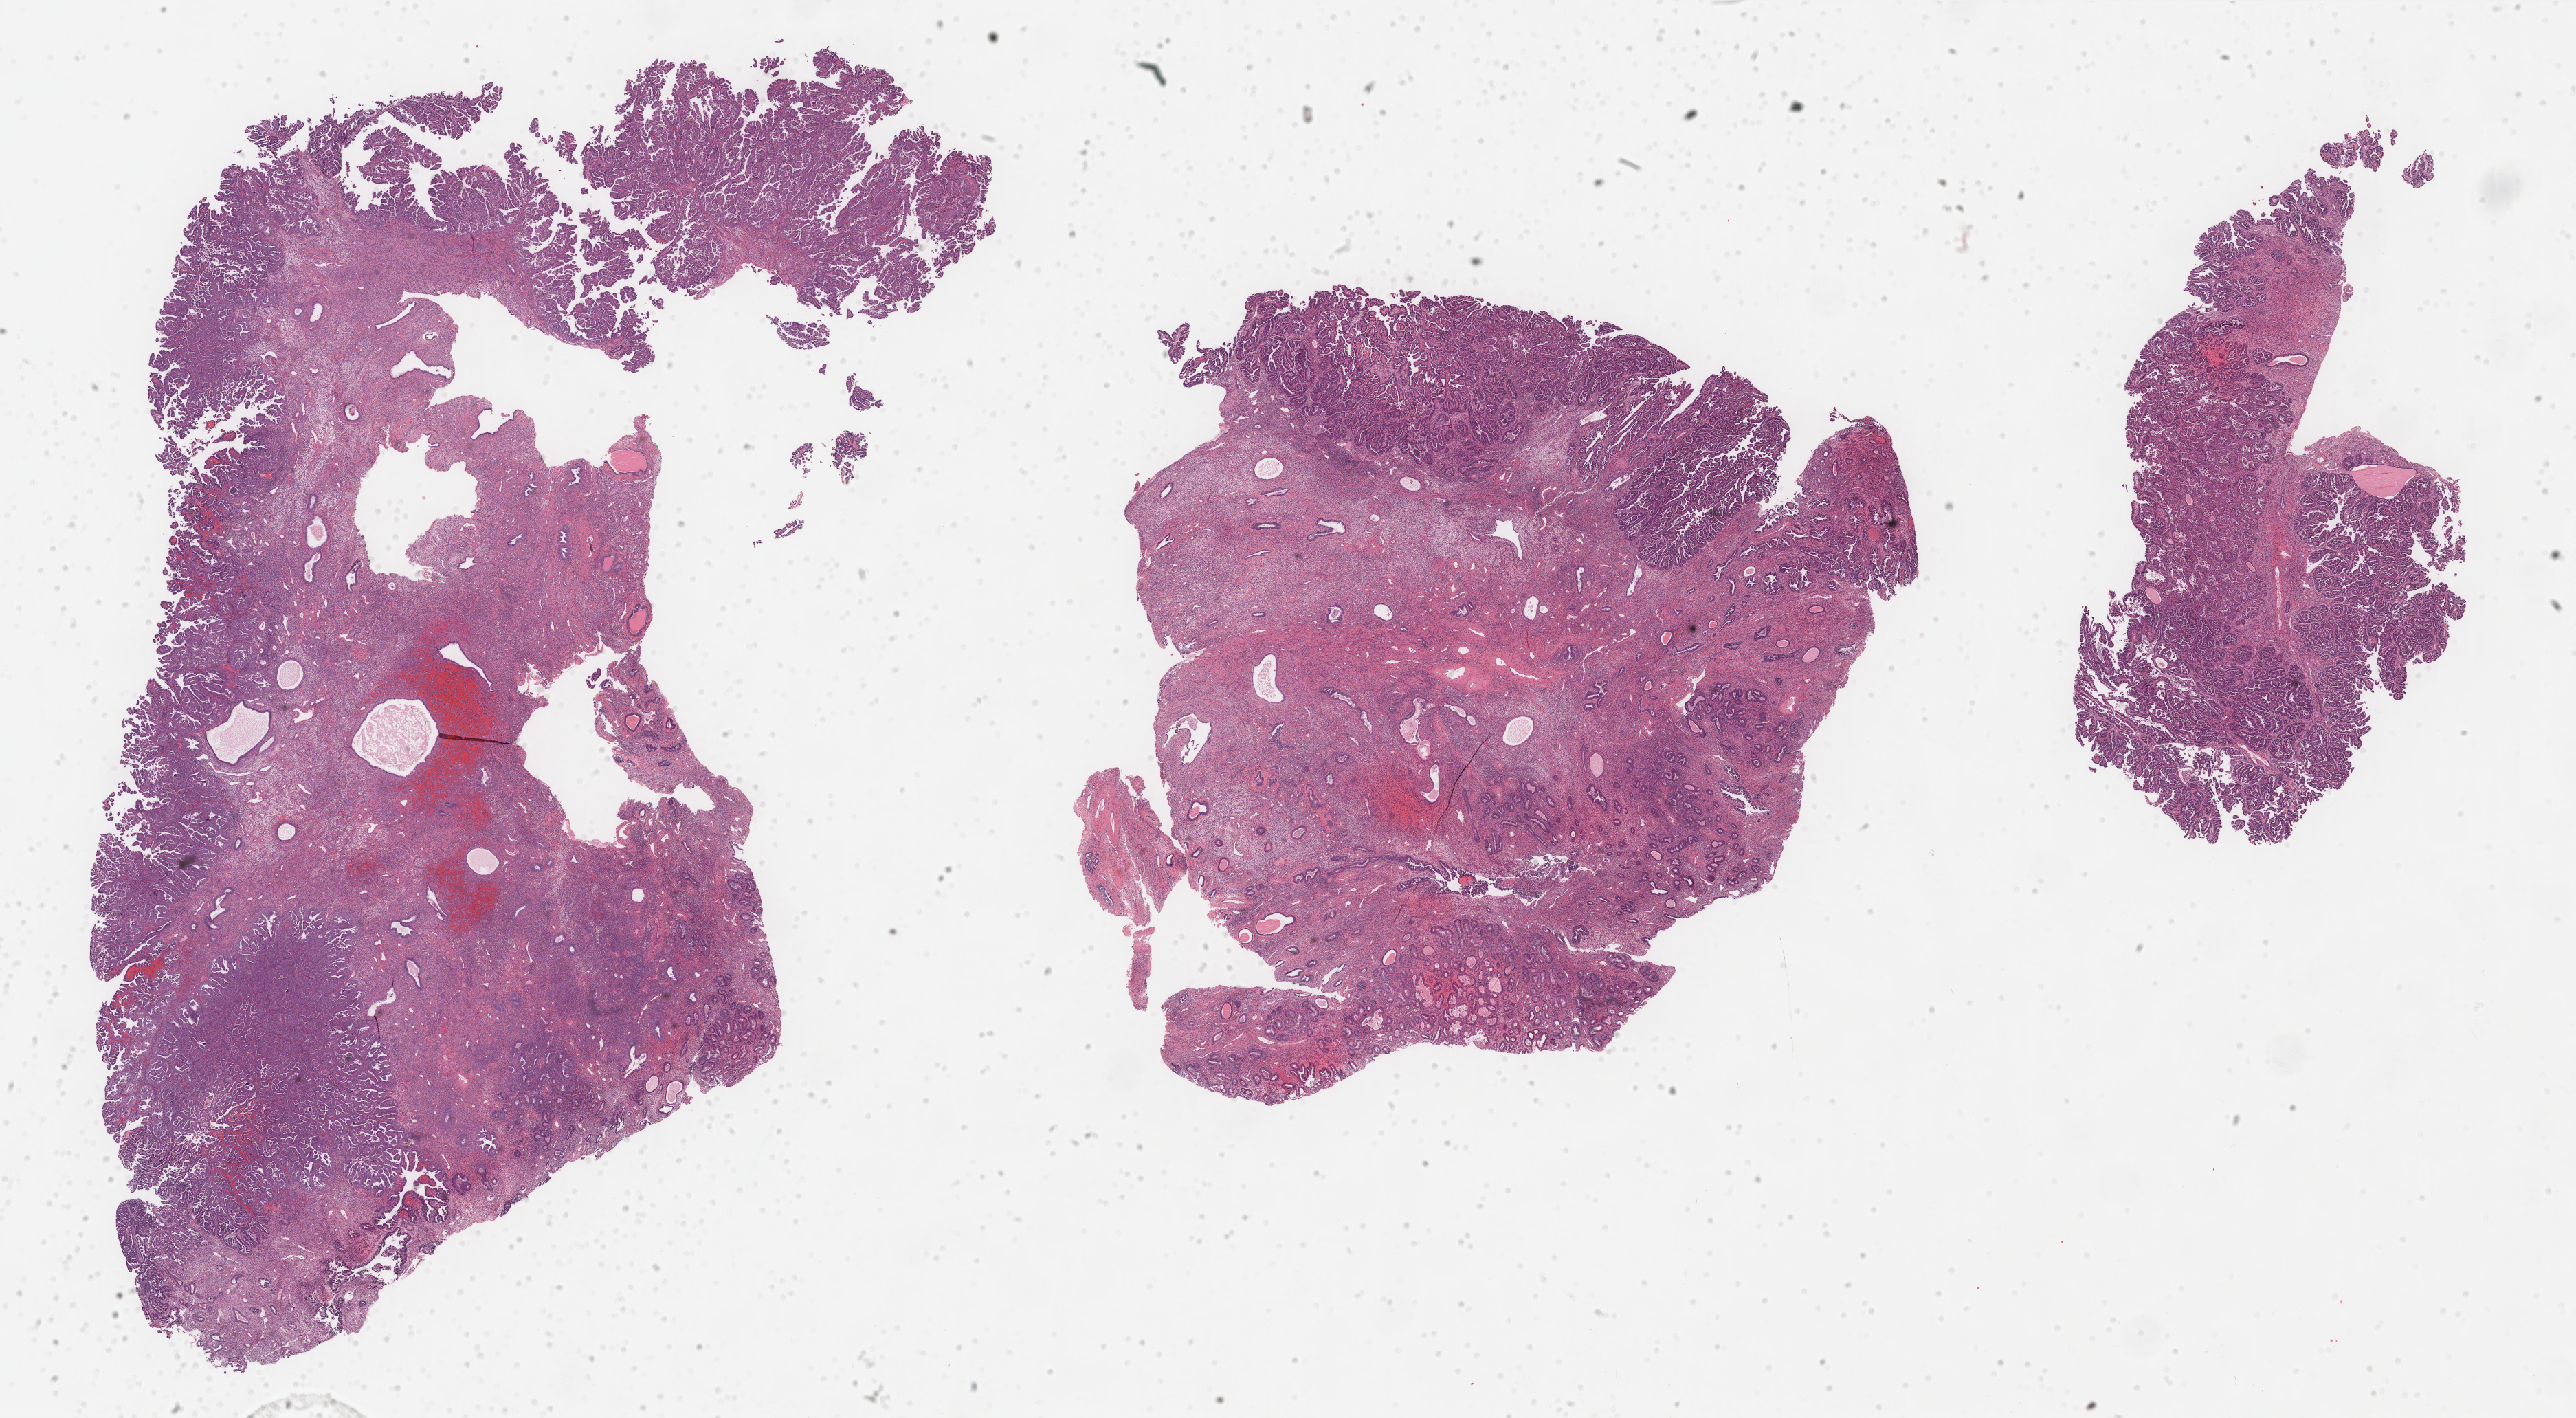
Digitized H&E-stained tissue section (whole slide), whole scanned area (about 29.7 x 16.4 mm) shown as a low-resolution overview, FFPE section, primary tumour sample from the uterus. Female, age 65 years at initial diagnosis. Histologic grade: G3 (poorly differentiated).
- FIGO stage: IB
- diagnosis: Serous cystadenocarcinoma, NOS (endometrium)